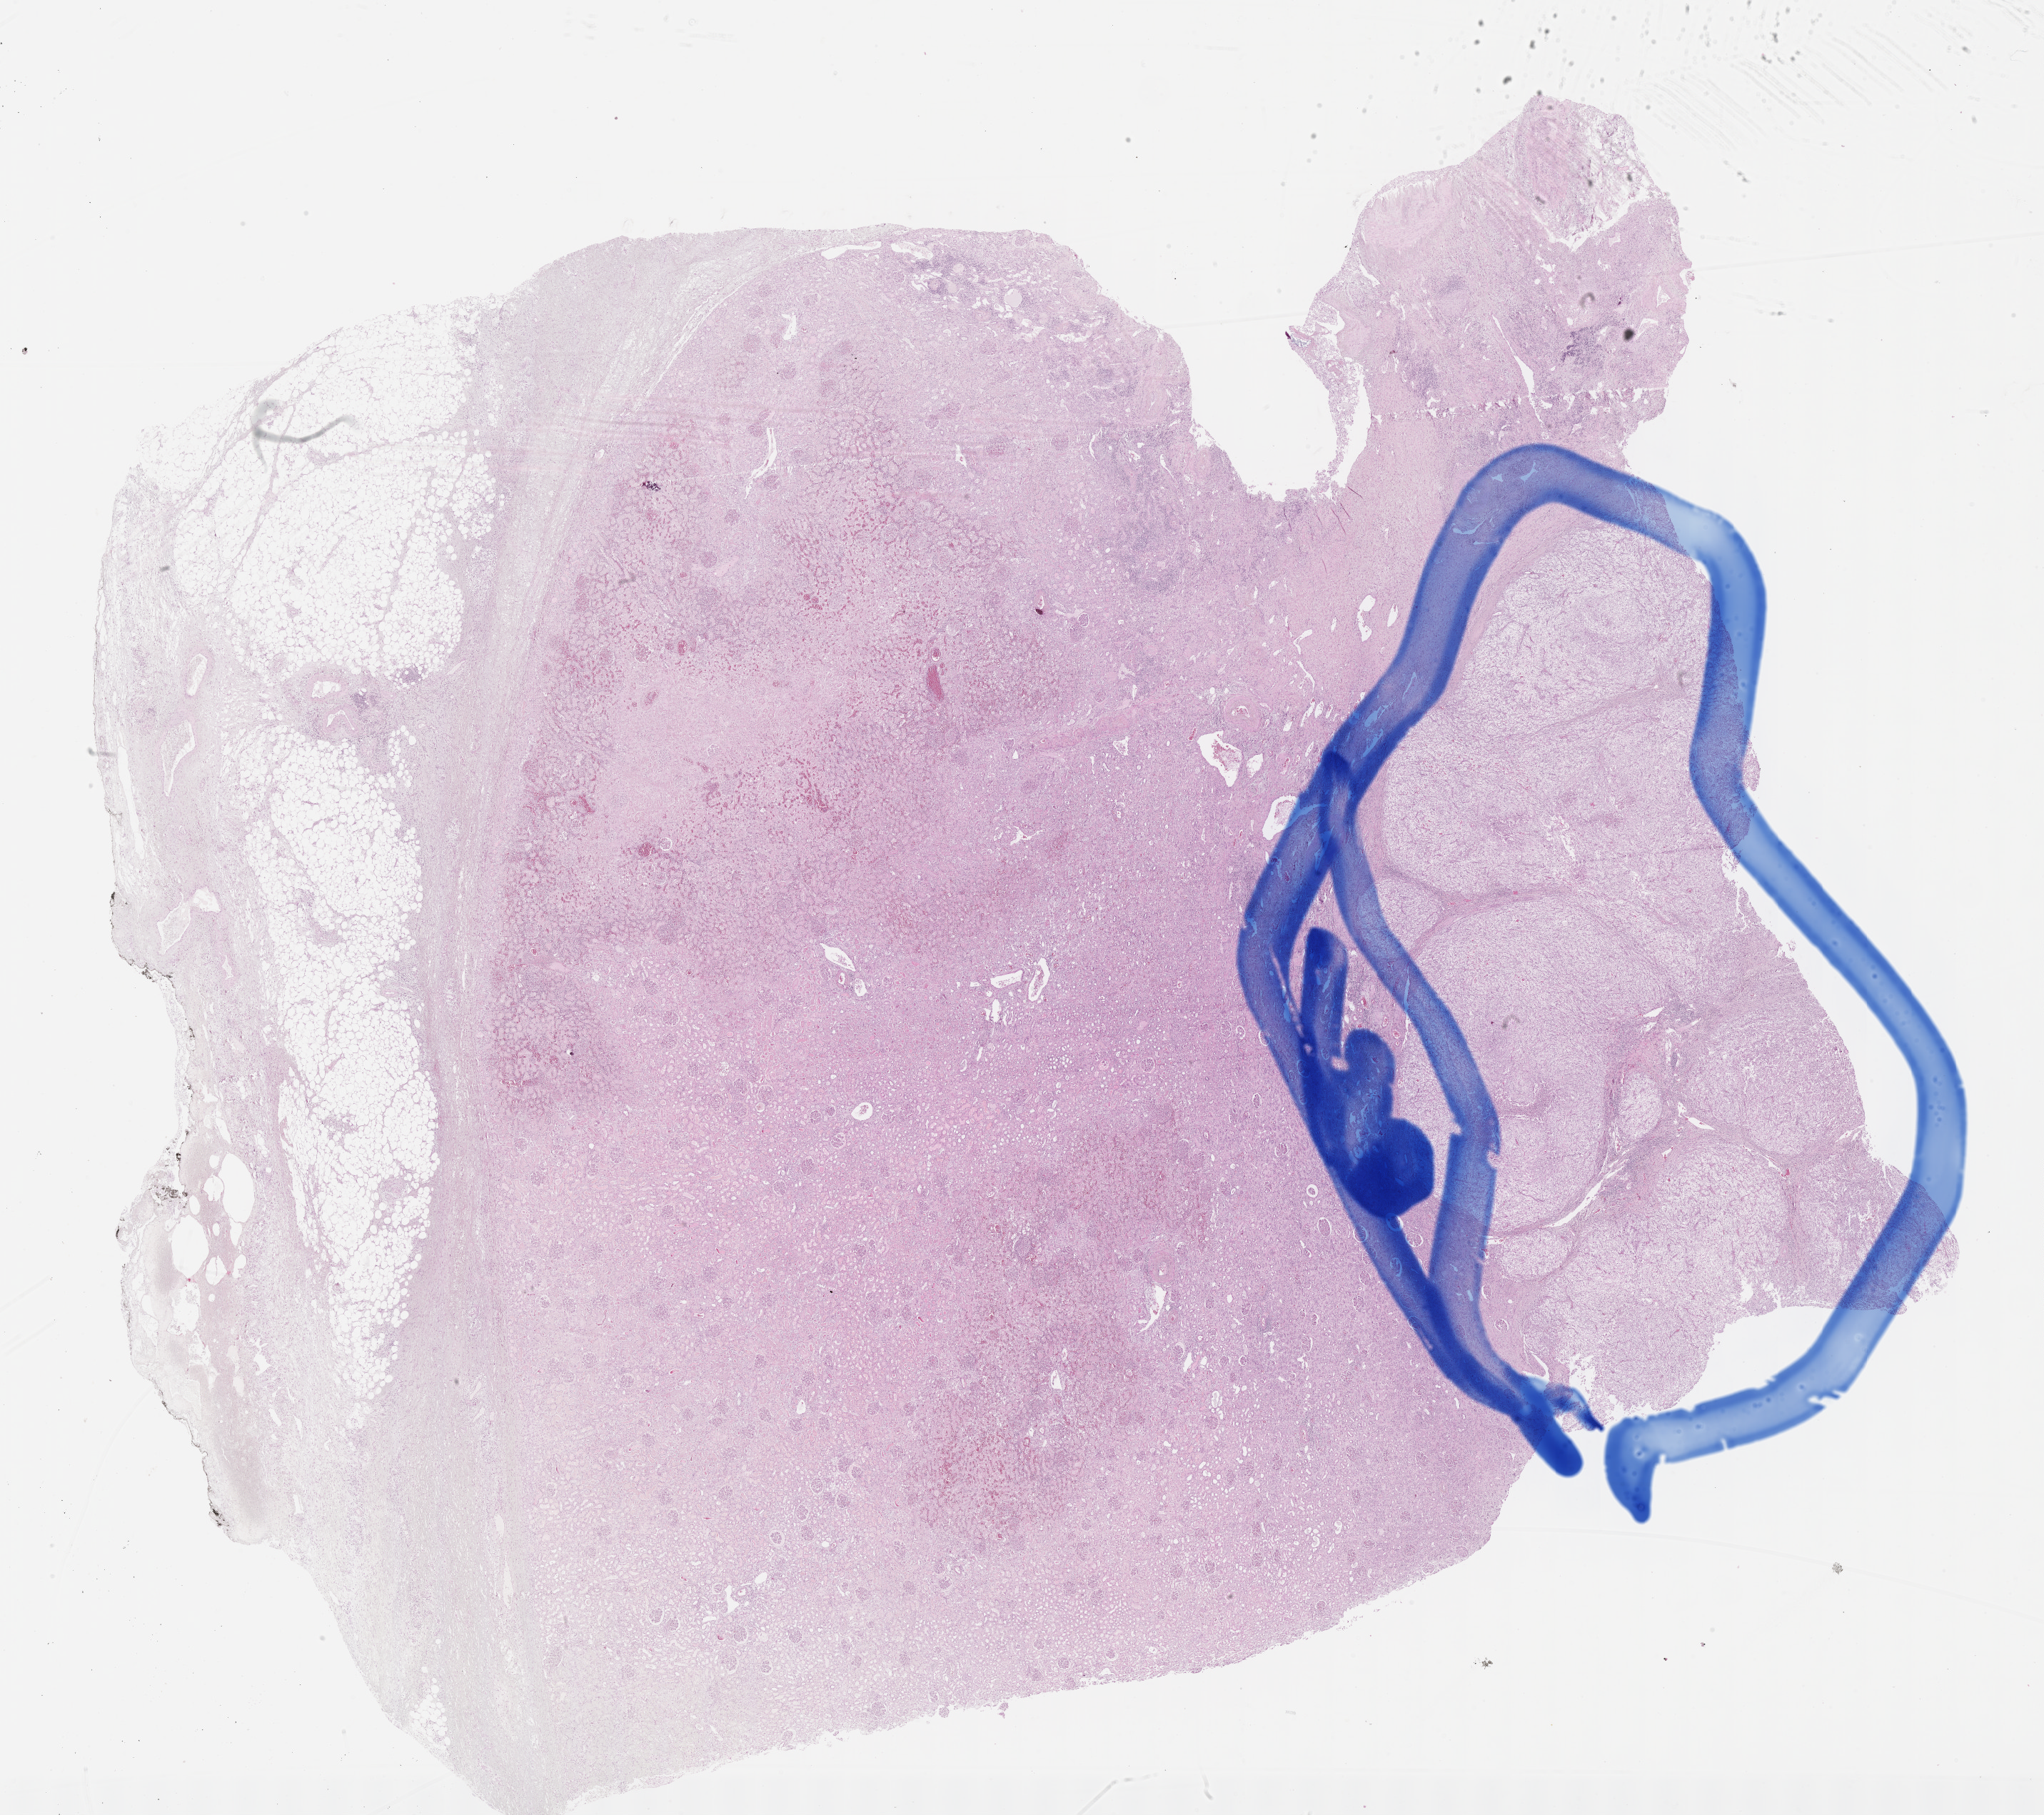
Digitized H&E-stained tissue section (whole slide), low-resolution overview of the scanned area, about 23.1 x 20.6 mm, FFPE section, primary tumour sample from the kidney. Female, age 57 years at initial diagnosis. Histologic grade: G4 (undifferentiated).
Lymph nodes positive (case pathology): 0 of 5 examined. Histologic diagnosis: Clear cell adenocarcinoma, NOS. AJCC pathologic stage: III.